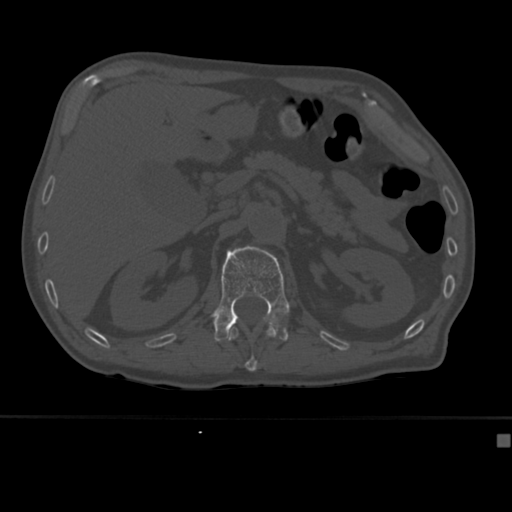
CT including the spine, one axial slice; position 175 of 430 along the scan axis; reconstruction kernel Br40s; 120 kVp; bone window (W 1800 / L 400 HU); 1.5 mm slice thickness; 512 × 512 image matrix, field of view 337 × 337 mm. Male patient, age 64 years. From the clinical record (not read from this slice): primary cancer: uterus; vertebrae with lytic lesions (as recorded): T1, T4, T5, T7, L5.
Outlined on this slice (semi-automatically segmented with operator editing):
- L1 vertebra: box from (x=212, y=246) to (x=290, y=342) px
- T12 vertebra: (x=229, y=320)–(x=277, y=372)